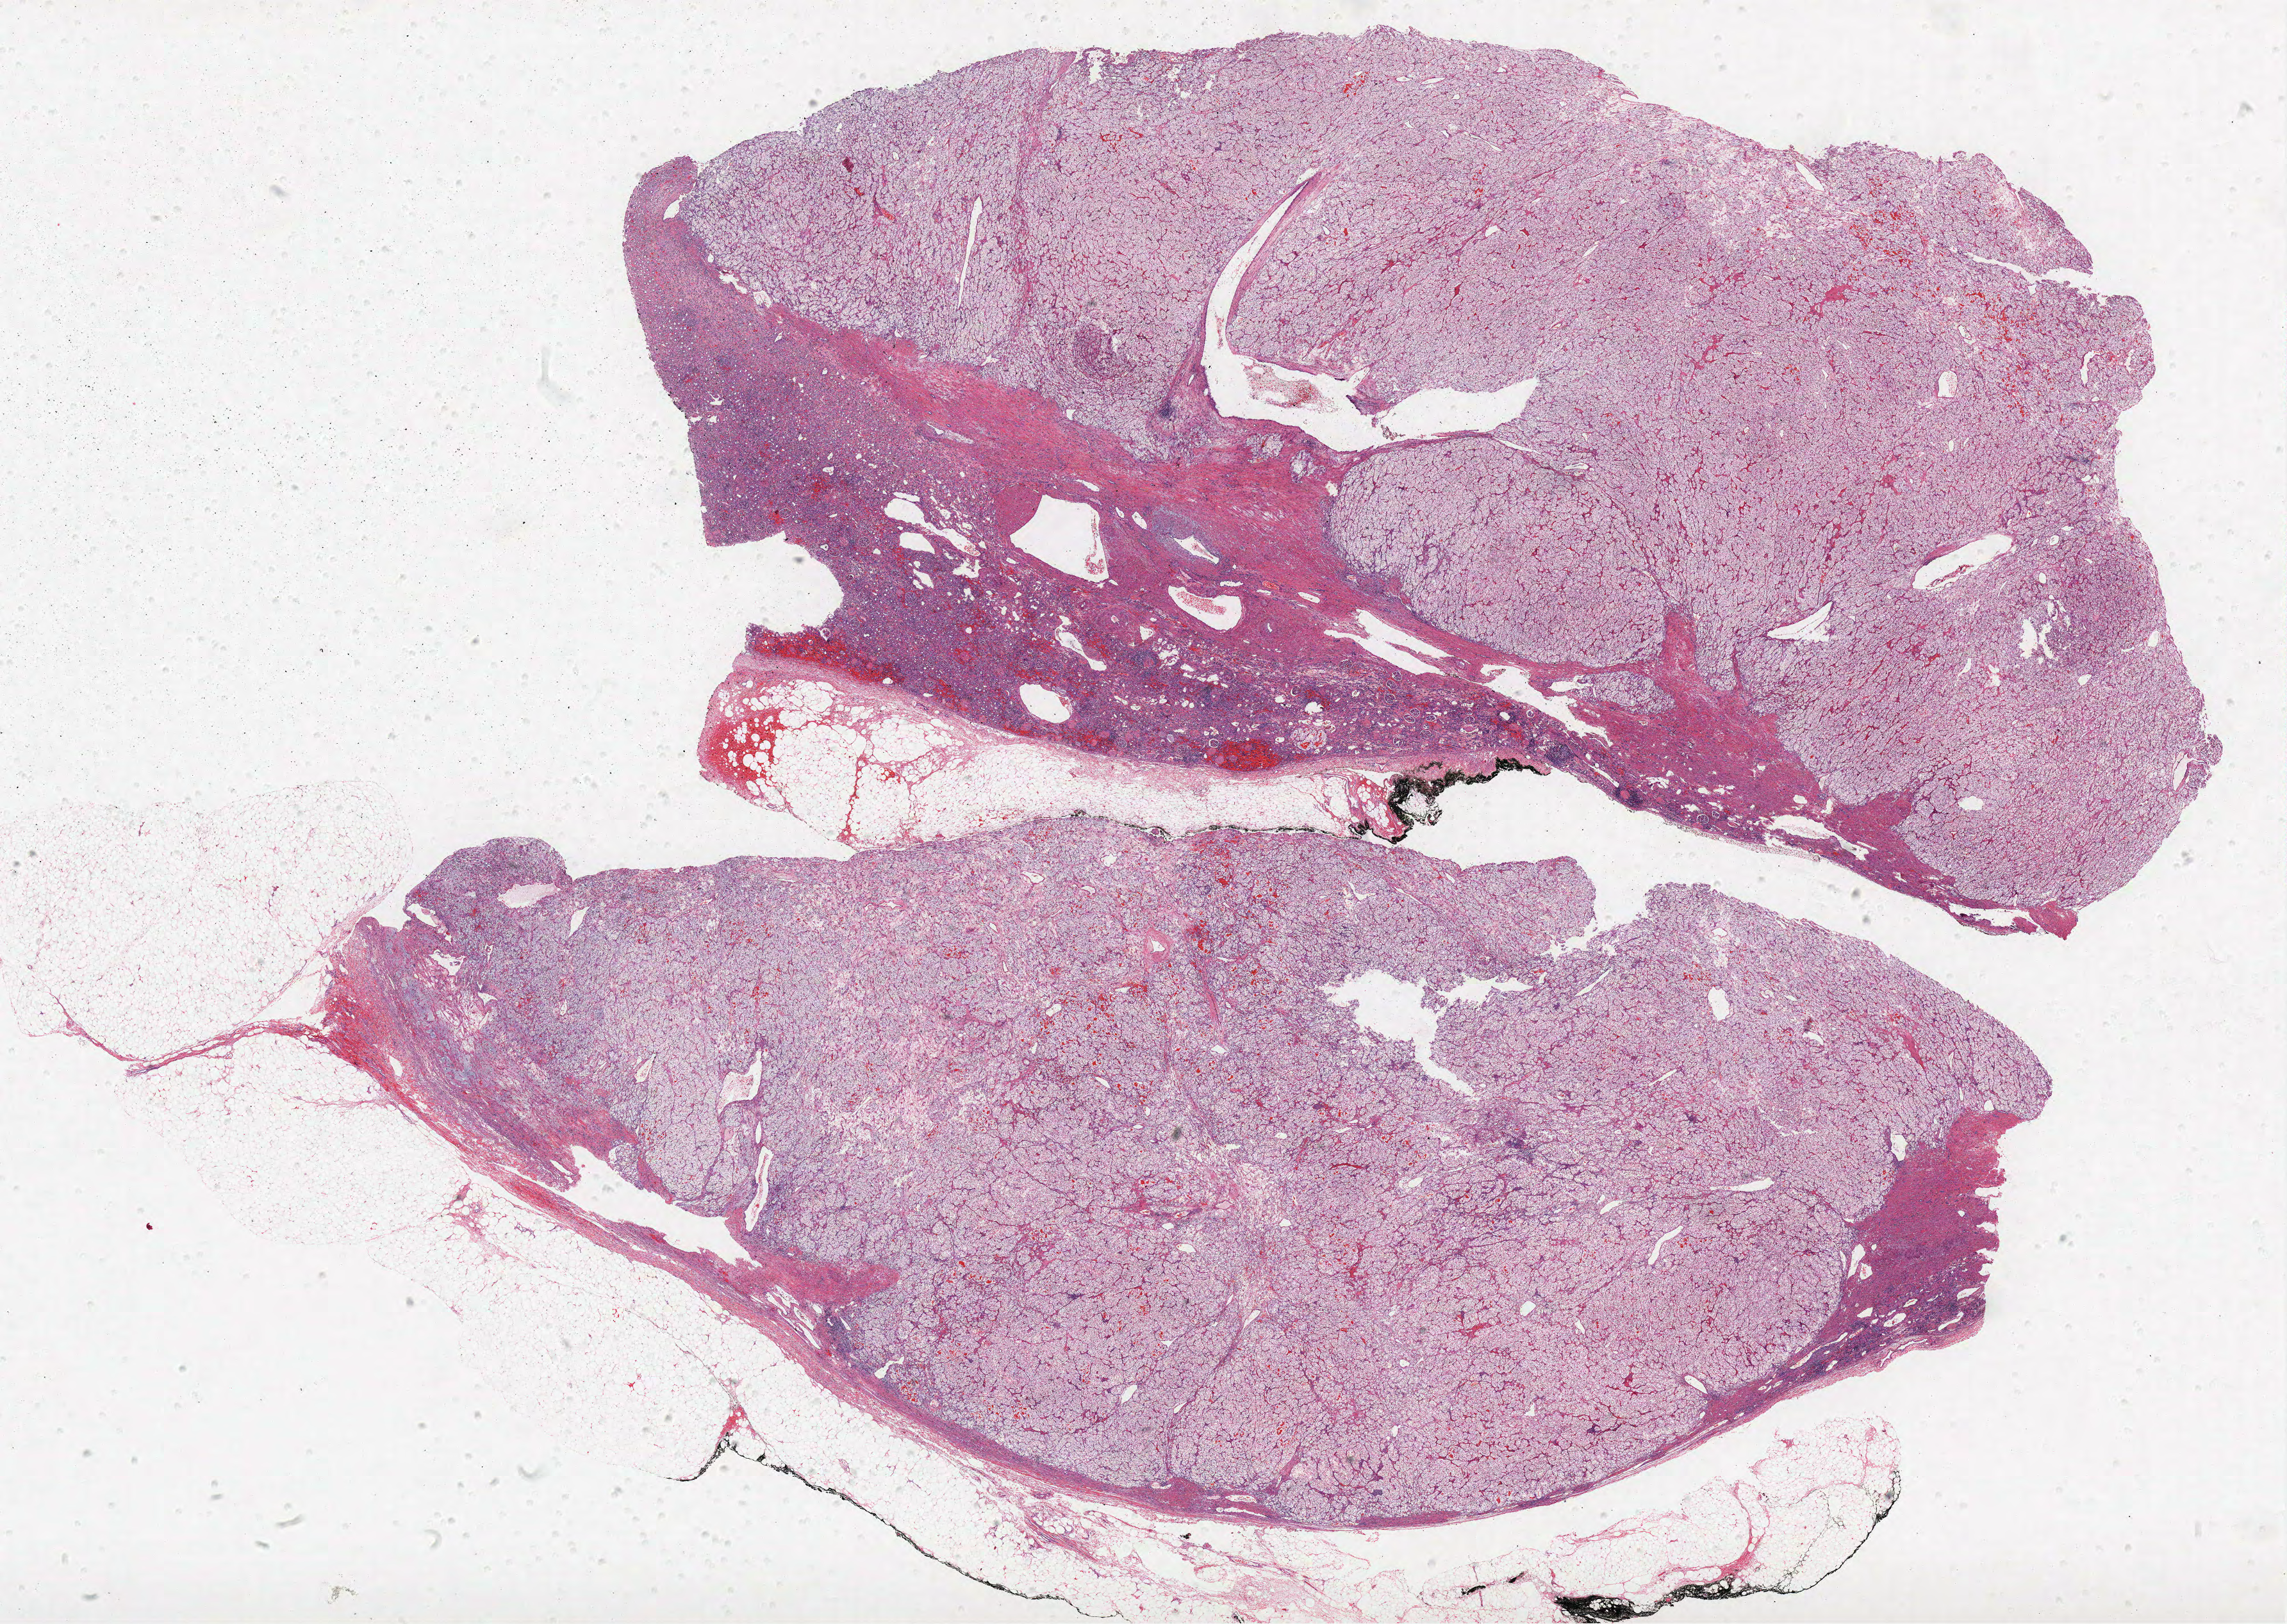
H&E-stained whole-slide image, low-resolution overview of the scanned area, about 28.5 x 20.3 mm. FFPE section. Primary tumour sample from the kidney. Patient: female, age at initial diagnosis 64 years. Histologic grade: G2 (moderately differentiated).
- AJCC pathologic stage: I
- diagnosis: Clear cell adenocarcinoma, NOS